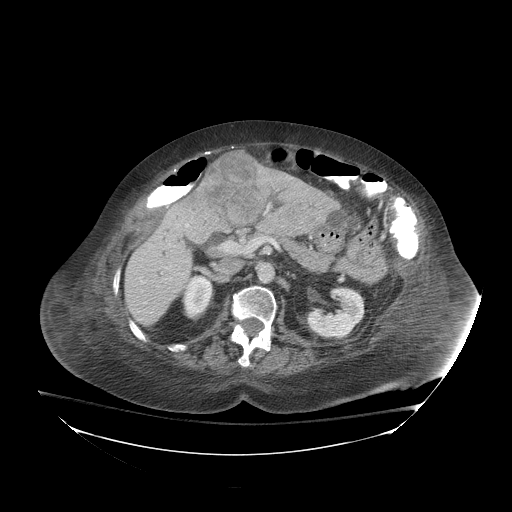
Contrast-enhanced abdominal CT (liver protocol), one axial slice; slice 37 of 81 in the series (ordered by position); reconstruction kernel STANDARD; soft-tissue window (W 400 / L 40 HU); 2.5 mm slice thickness; 512 × 512 image matrix, field of view 500 × 500 mm. From the clinical record (not read from this slice): diagnosis: hepatocellular carcinoma (patient treated with transarterial chemoembolisation; whether this scan precedes or follows treatment is not stated here); TNM stage (as recorded): Stage-I; Child-Pugh class: B.
Structures marked on this image (semi-automatic segmentation, software-assisted and operator-edited):
- liver parenchyma outside the tumour (the mass and vessels are separate outlines, so this box may not span the whole liver): bounding box (x1, y1, x2, y2) in pixels: (124, 176, 338, 326)
- mass: (200, 149, 265, 225)
- liver vessels: (186, 224, 189, 227)